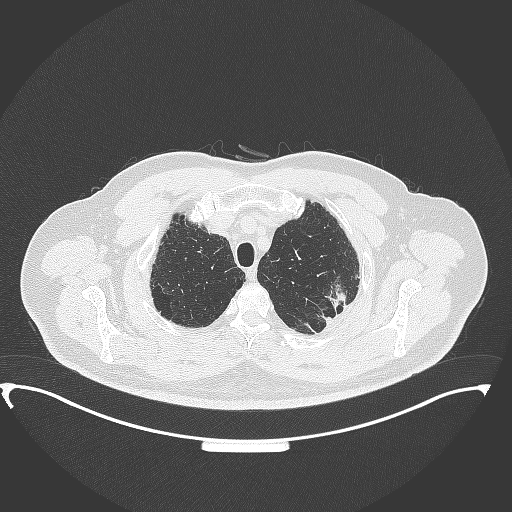
Chest CT, one axial slice; slice 311 of 350 in the series (ordered by position); reconstruction kernel B70f; 120 kVp; lung window (W 1500 / L -600 HU); 512 × 512 image matrix, field of view 459 × 459 mm. Male patient, age 64 years. Case-level facts recorded for this patient, not image findings: clinical TNM (as recorded): T1c N1 M1.
Outlined on this slice (rectangle marked by the reading radiologist):
- lung tumour (recorded histology: adenocarcinoma): bounding box (x1, y1, x2, y2) in pixels: (322, 273, 351, 315)